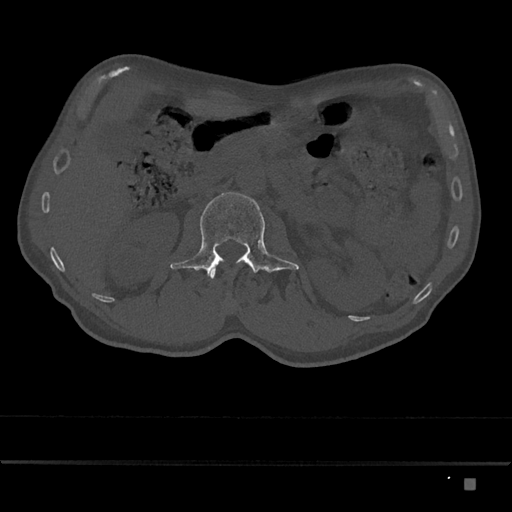
CT including the spine, one axial slice; slice 488 of 797 in the series (ordered by position); bone window (W 1800 / L 400 HU); 0.5 mm slice thickness; 512 × 512 image matrix, field of view 390 × 390 mm. Male patient, age 72 years. From the clinical record (not read from this slice): primary cancer: prostate.
Structures marked on this image (semi-automatically segmented with operator editing):
- L1 vertebra: bounding box <210,269,216,279> (left, top, right, bottom; pixels)
- L2 vertebra: <170,192,299,276>